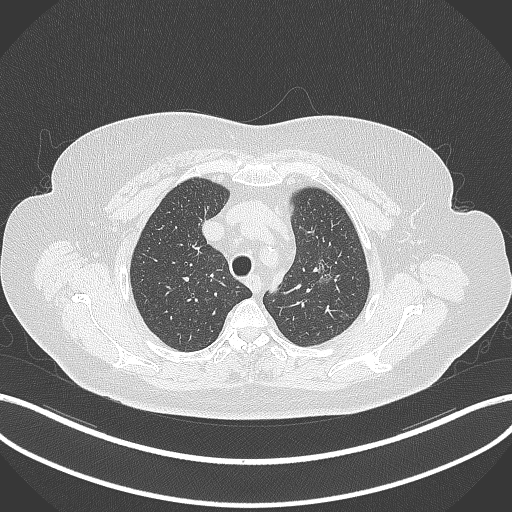
Chest CT, one axial slice. Slice 269 of 309 in the series (ordered by position). 120 kVp. Lung window (W 1500 / L -600 HU). 512 × 512 image matrix, field of view 400 × 400 mm. Patient: female, 70 years. From the clinical record (not read from this slice): clinical TNM (as recorded): T1c N0 M0.
Annotated regions visible in this slice (rectangle marked by the reading radiologist):
- lung tumour (recorded histology: adenocarcinoma): bounding box [x1, y1, x2, y2] px = [312, 255, 336, 288]